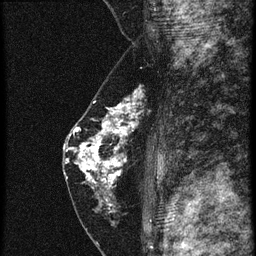
Breast MRI (dynamic contrast-enhanced), one sagittal slice; position 33 of 60 along the scan axis; 4 images stored at this slice position (order not interpretable as contrast timing); 1.5 T; TE 4.2 ms, TR 20.4 ms; 1.5 mm slice thickness; 256 × 256 image matrix, field of view 180 × 180 mm. Patient: female, 46 years. Case-level facts recorded for this patient, not image findings: setting: breast cancer imaged before/during neoadjuvant chemotherapy; receptor status: triple-negative.
Outlined on this slice (semi-automatically segmented with operator editing):
- analysis volume of interest (the breast-tissue region the enhancement analysis was run in; not a lesion): bounding box [x1, y1, x2, y2] px = [67, 88, 153, 201]
- tumour enhancement mask (voxels above the 90 % enhancement threshold inside the analysis volume of interest): [67, 96, 138, 201]